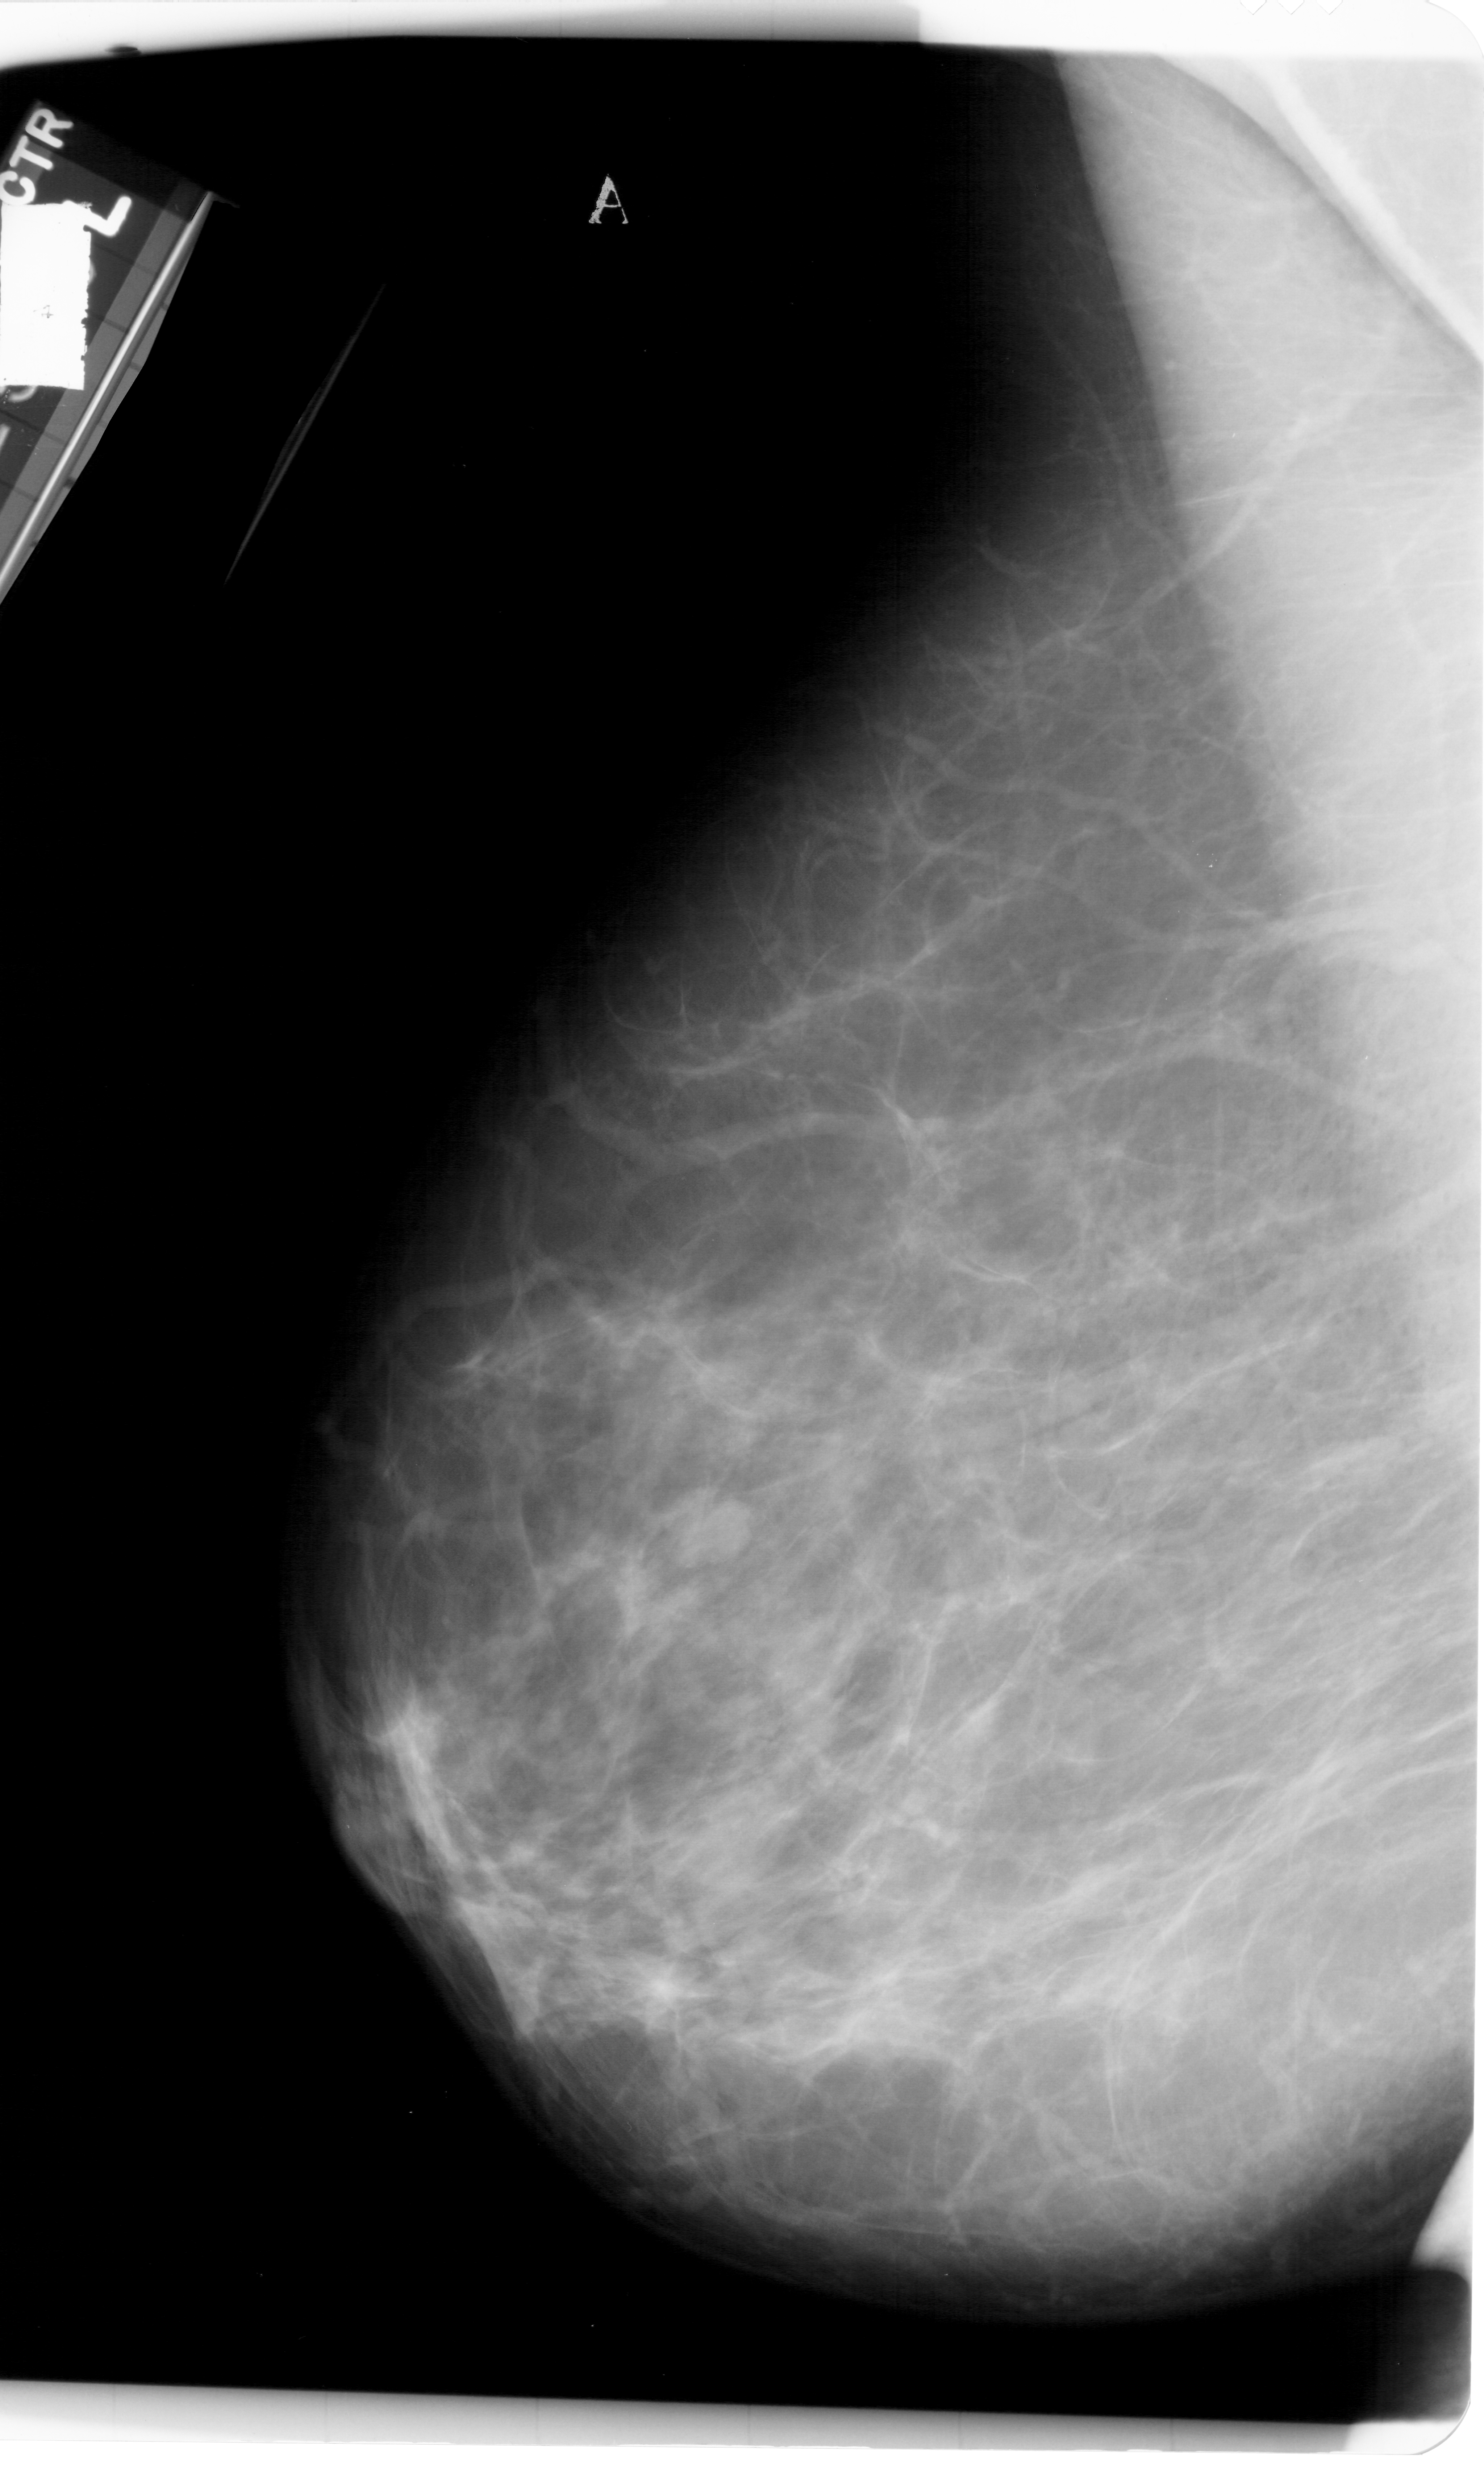
Scanned film-screen mammogram. Left breast. Mediolateral oblique (MLO) view. 1484 × 2490 image matrix.
Expert-marked regions of interest on this film, with their recorded descriptors:
- mass, shape lobulated, margins circumscribed; BI-RADS assessment category 4; subtlety rating 3 on a 1 (subtle) to 5 (obvious) scale; pathology result (as recorded, not read from the image): benign: bounding box (x1, y1, x2, y2) in pixels: (668, 1486, 750, 1568)